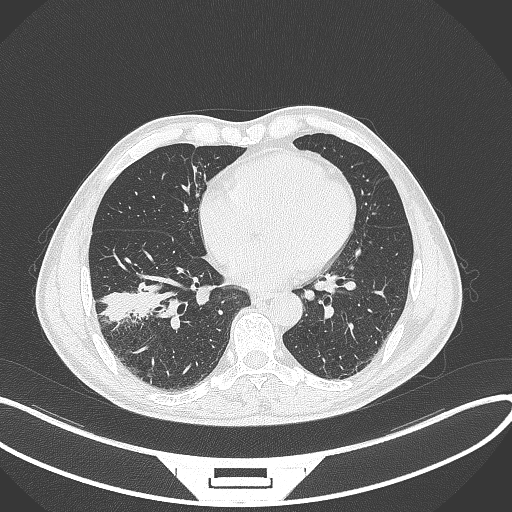
Chest CT, one axial slice. Position 141 of 364 along the scan axis. Lung window (W 1500 / L -600 HU). 1 mm slice thickness. 512 × 512 image matrix, field of view 400 × 400 mm. Male patient, age 58 years. From the clinical record (not read from this slice): clinical TNM (as recorded): T3 N0 M0.
Annotated regions visible in this slice (bounding box drawn by a radiologist):
- lung tumour (recorded histology: squamous cell carcinoma): bounding box [x1, y1, x2, y2] px = [98, 286, 165, 325]